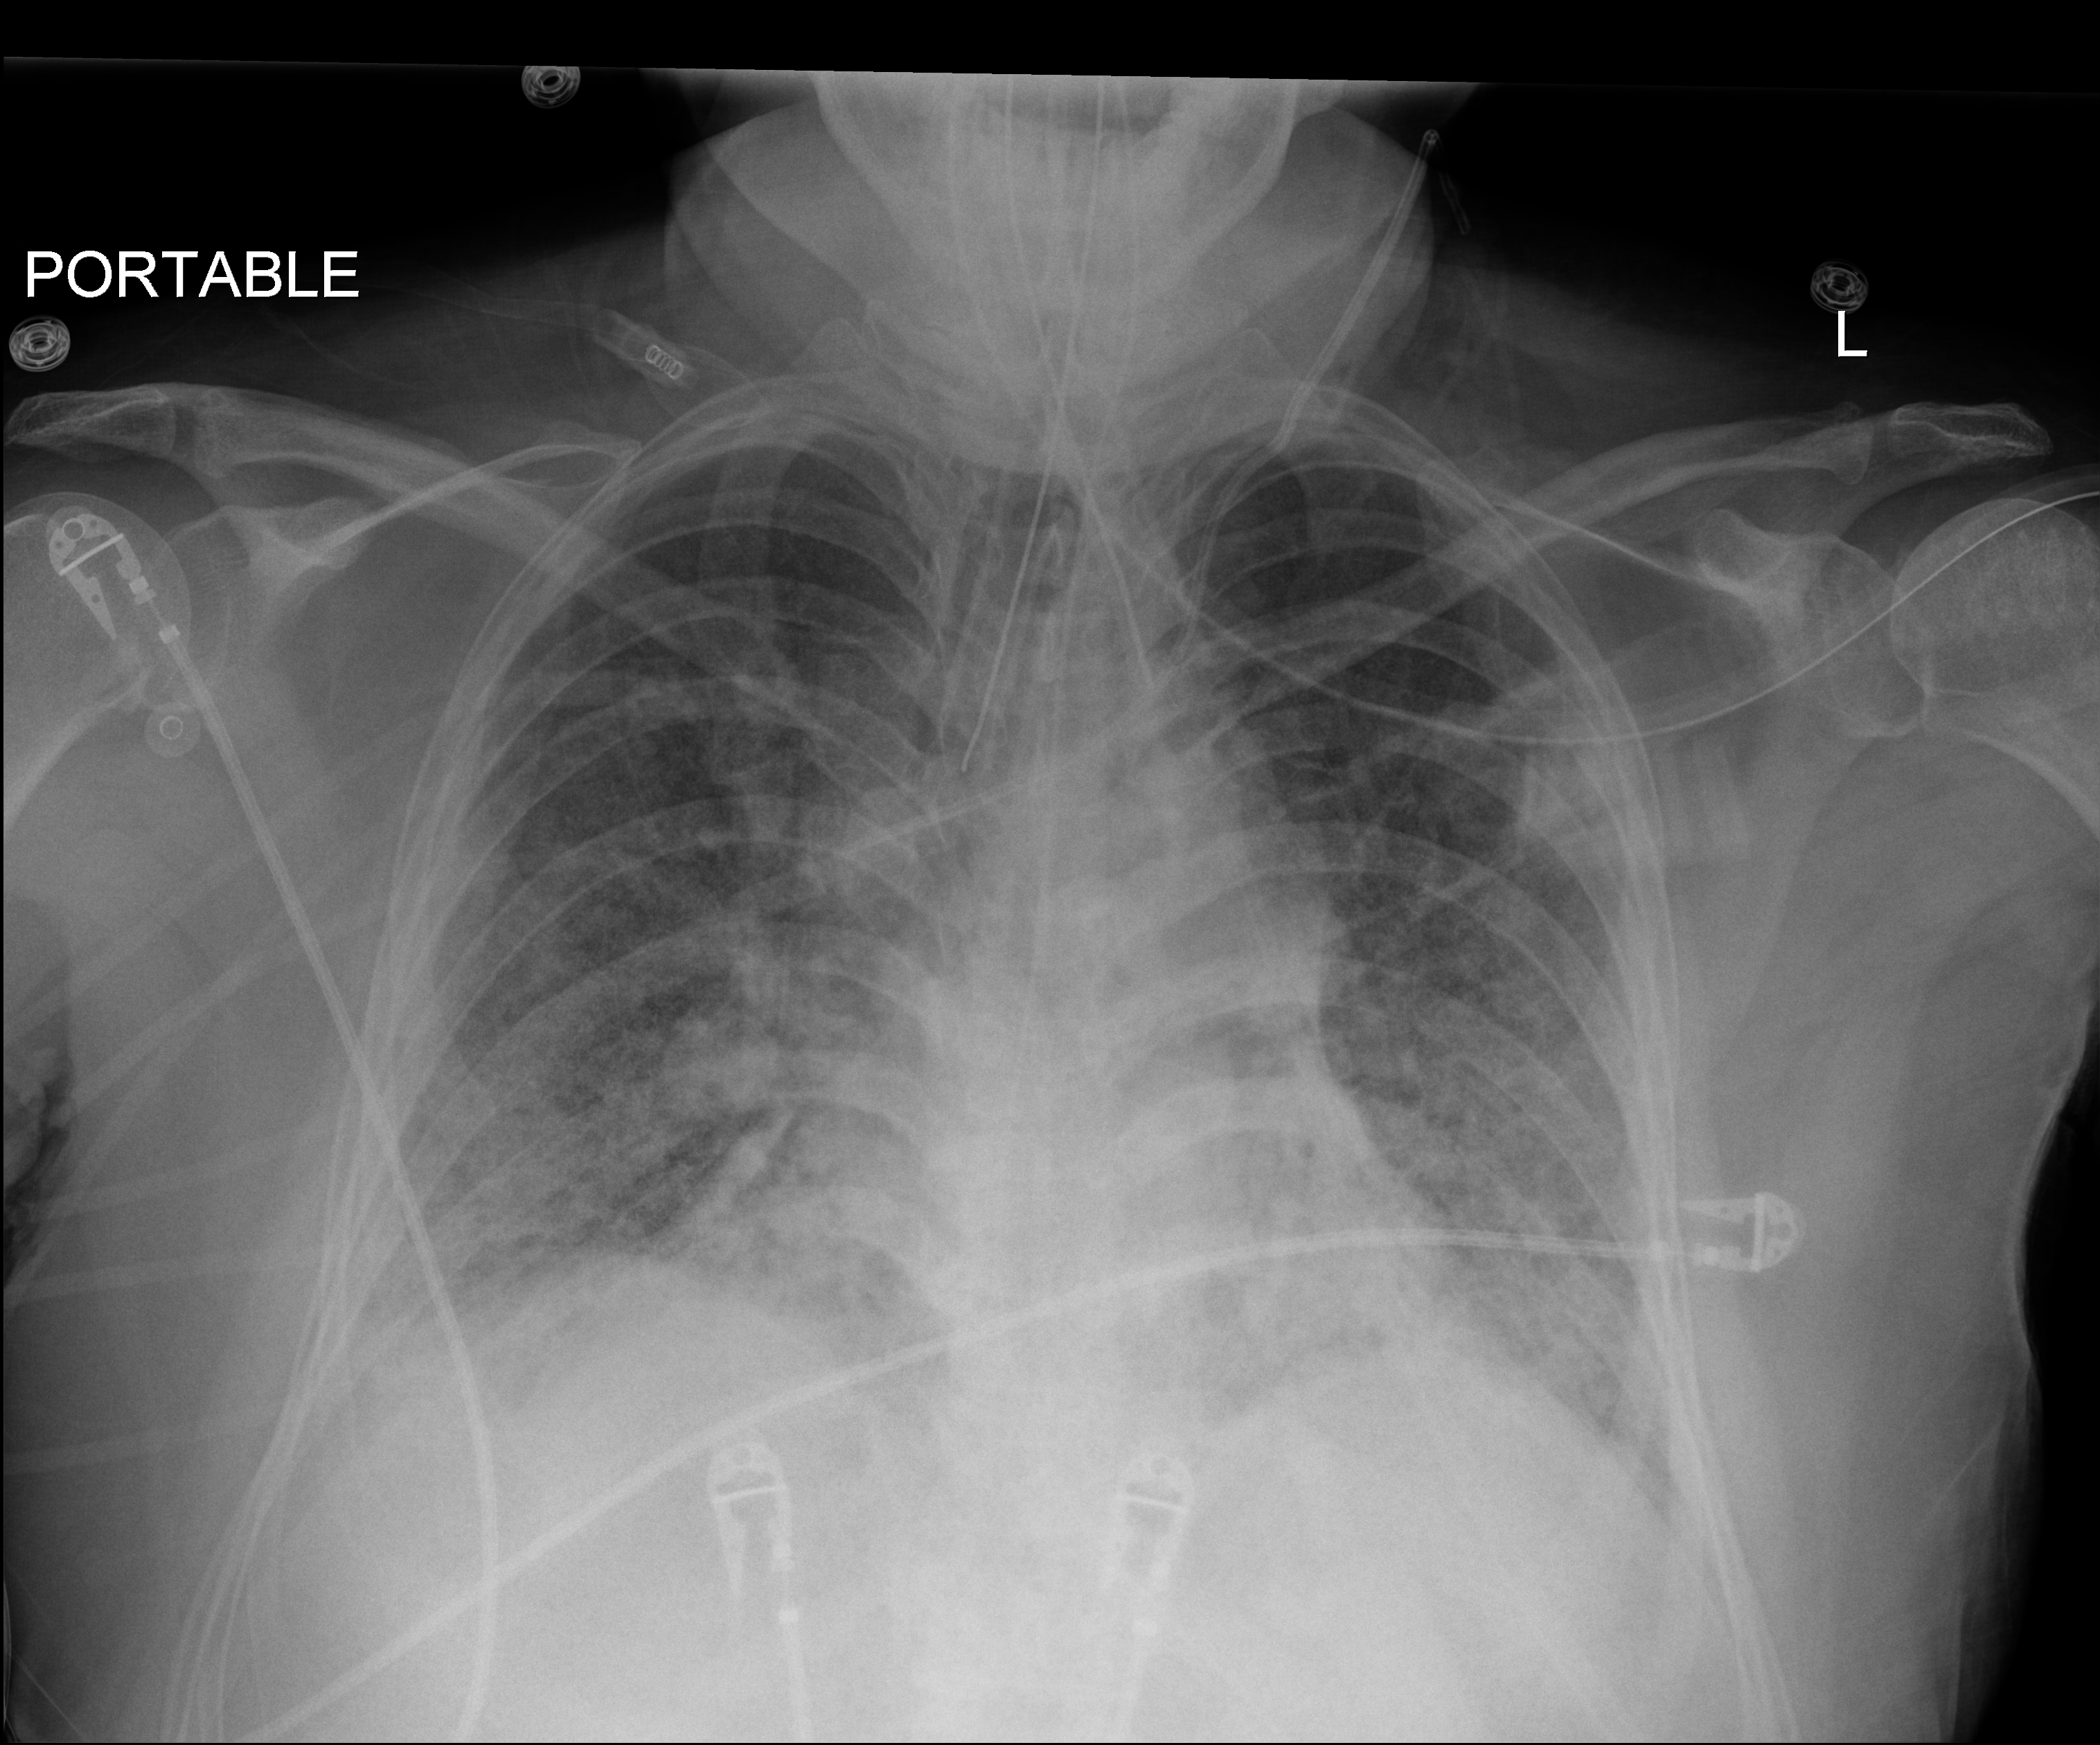
Chest X-ray (portable), anteroposterior (AP) projection. Adult patient hospitalised with COVID-19, age 18–59 years.
Hospital-stay facts (about this admission, not read from this image; timing relative to this image not recorded): admitted to intensive care during this hospital stay: yes; other chronic lung disease (admission record): no.